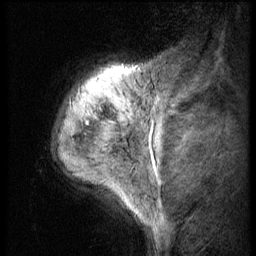
Breast MRI (dynamic contrast-enhanced), one sagittal slice; 3 images stored at this slice position (order not interpretable as contrast timing); 1.5 T; TE 4.2 ms, TR 9 ms; 2.5 mm slice thickness; 256 × 256 image matrix, field of view 180 × 180 mm. Female patient, age 50 years. Case-level facts recorded for this patient, not image findings: setting: breast cancer imaged before/during neoadjuvant chemotherapy; receptor status: triple-negative.
Annotated regions visible in this slice (semi-automatic segmentation, software-assisted and operator-edited):
- analysis volume of interest (the breast-tissue region the enhancement analysis was run in; not a lesion): box from (x=45, y=52) to (x=135, y=191) px
- tumour enhancement mask (voxels above the 140 % enhancement threshold inside the analysis volume of interest): (x=86, y=95)–(x=117, y=126)